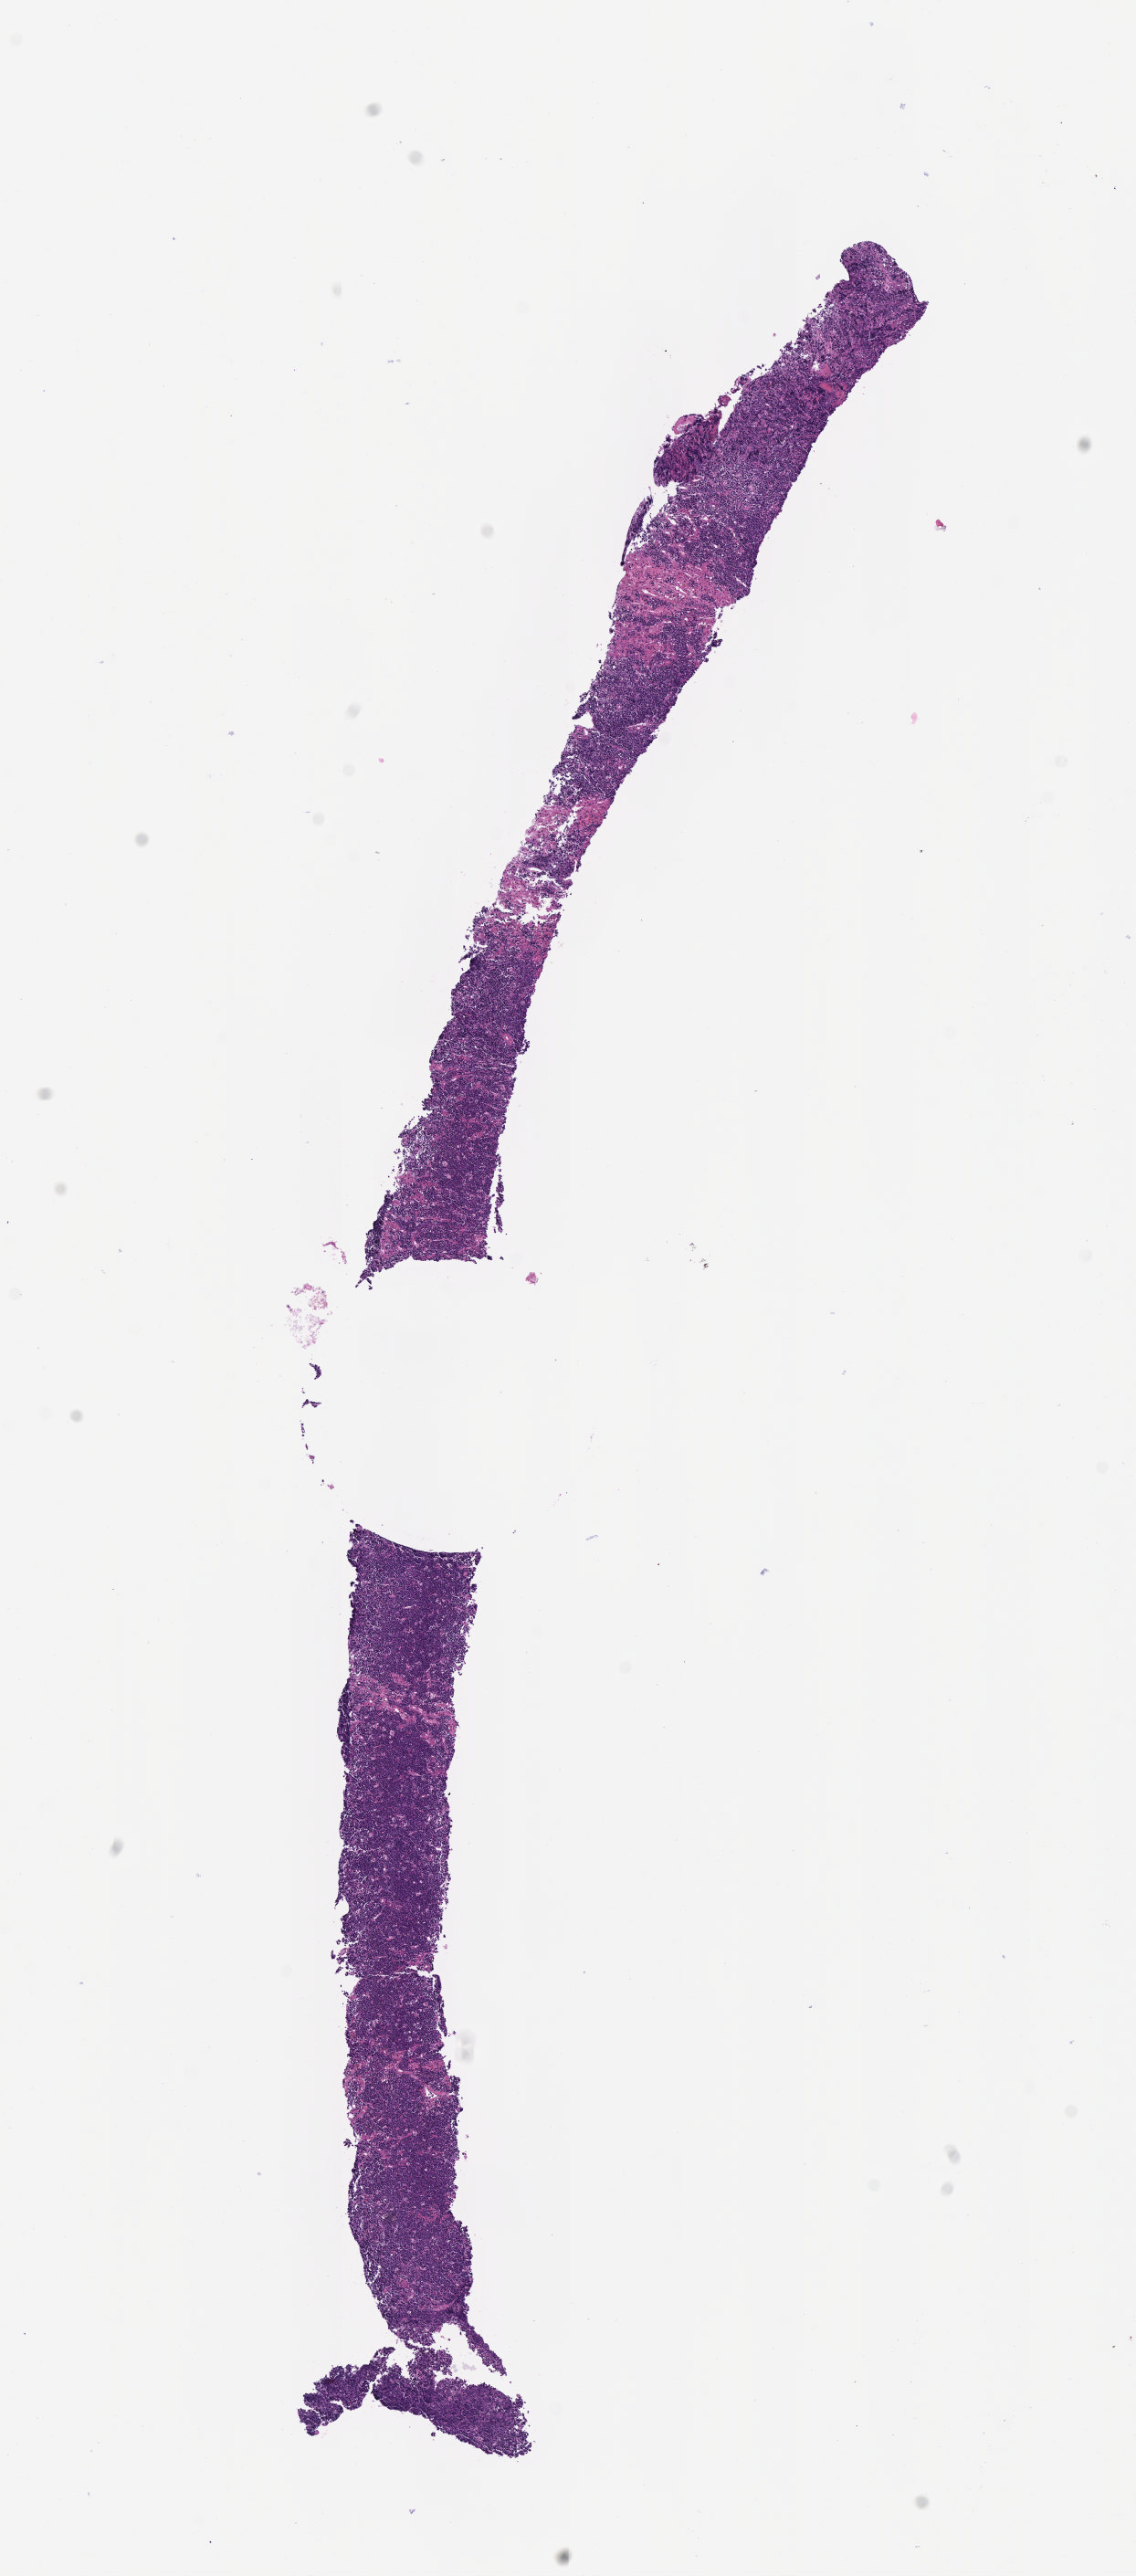
H&E whole-slide image, low-resolution overview of the scanned area, about 5.0 x 11.4 mm. Female patient. Slide review estimates, as recorded: tumor cells 90%, tumor nuclei 85%, stromal cells 5%, necrosis 0%, normal cells 5%. Infiltration values recorded for this section: lymphocyte infiltration 40%, monocyte infiltration 25%, neutrophil infiltration 5%.
* specimen: FFPE section; primary tumor